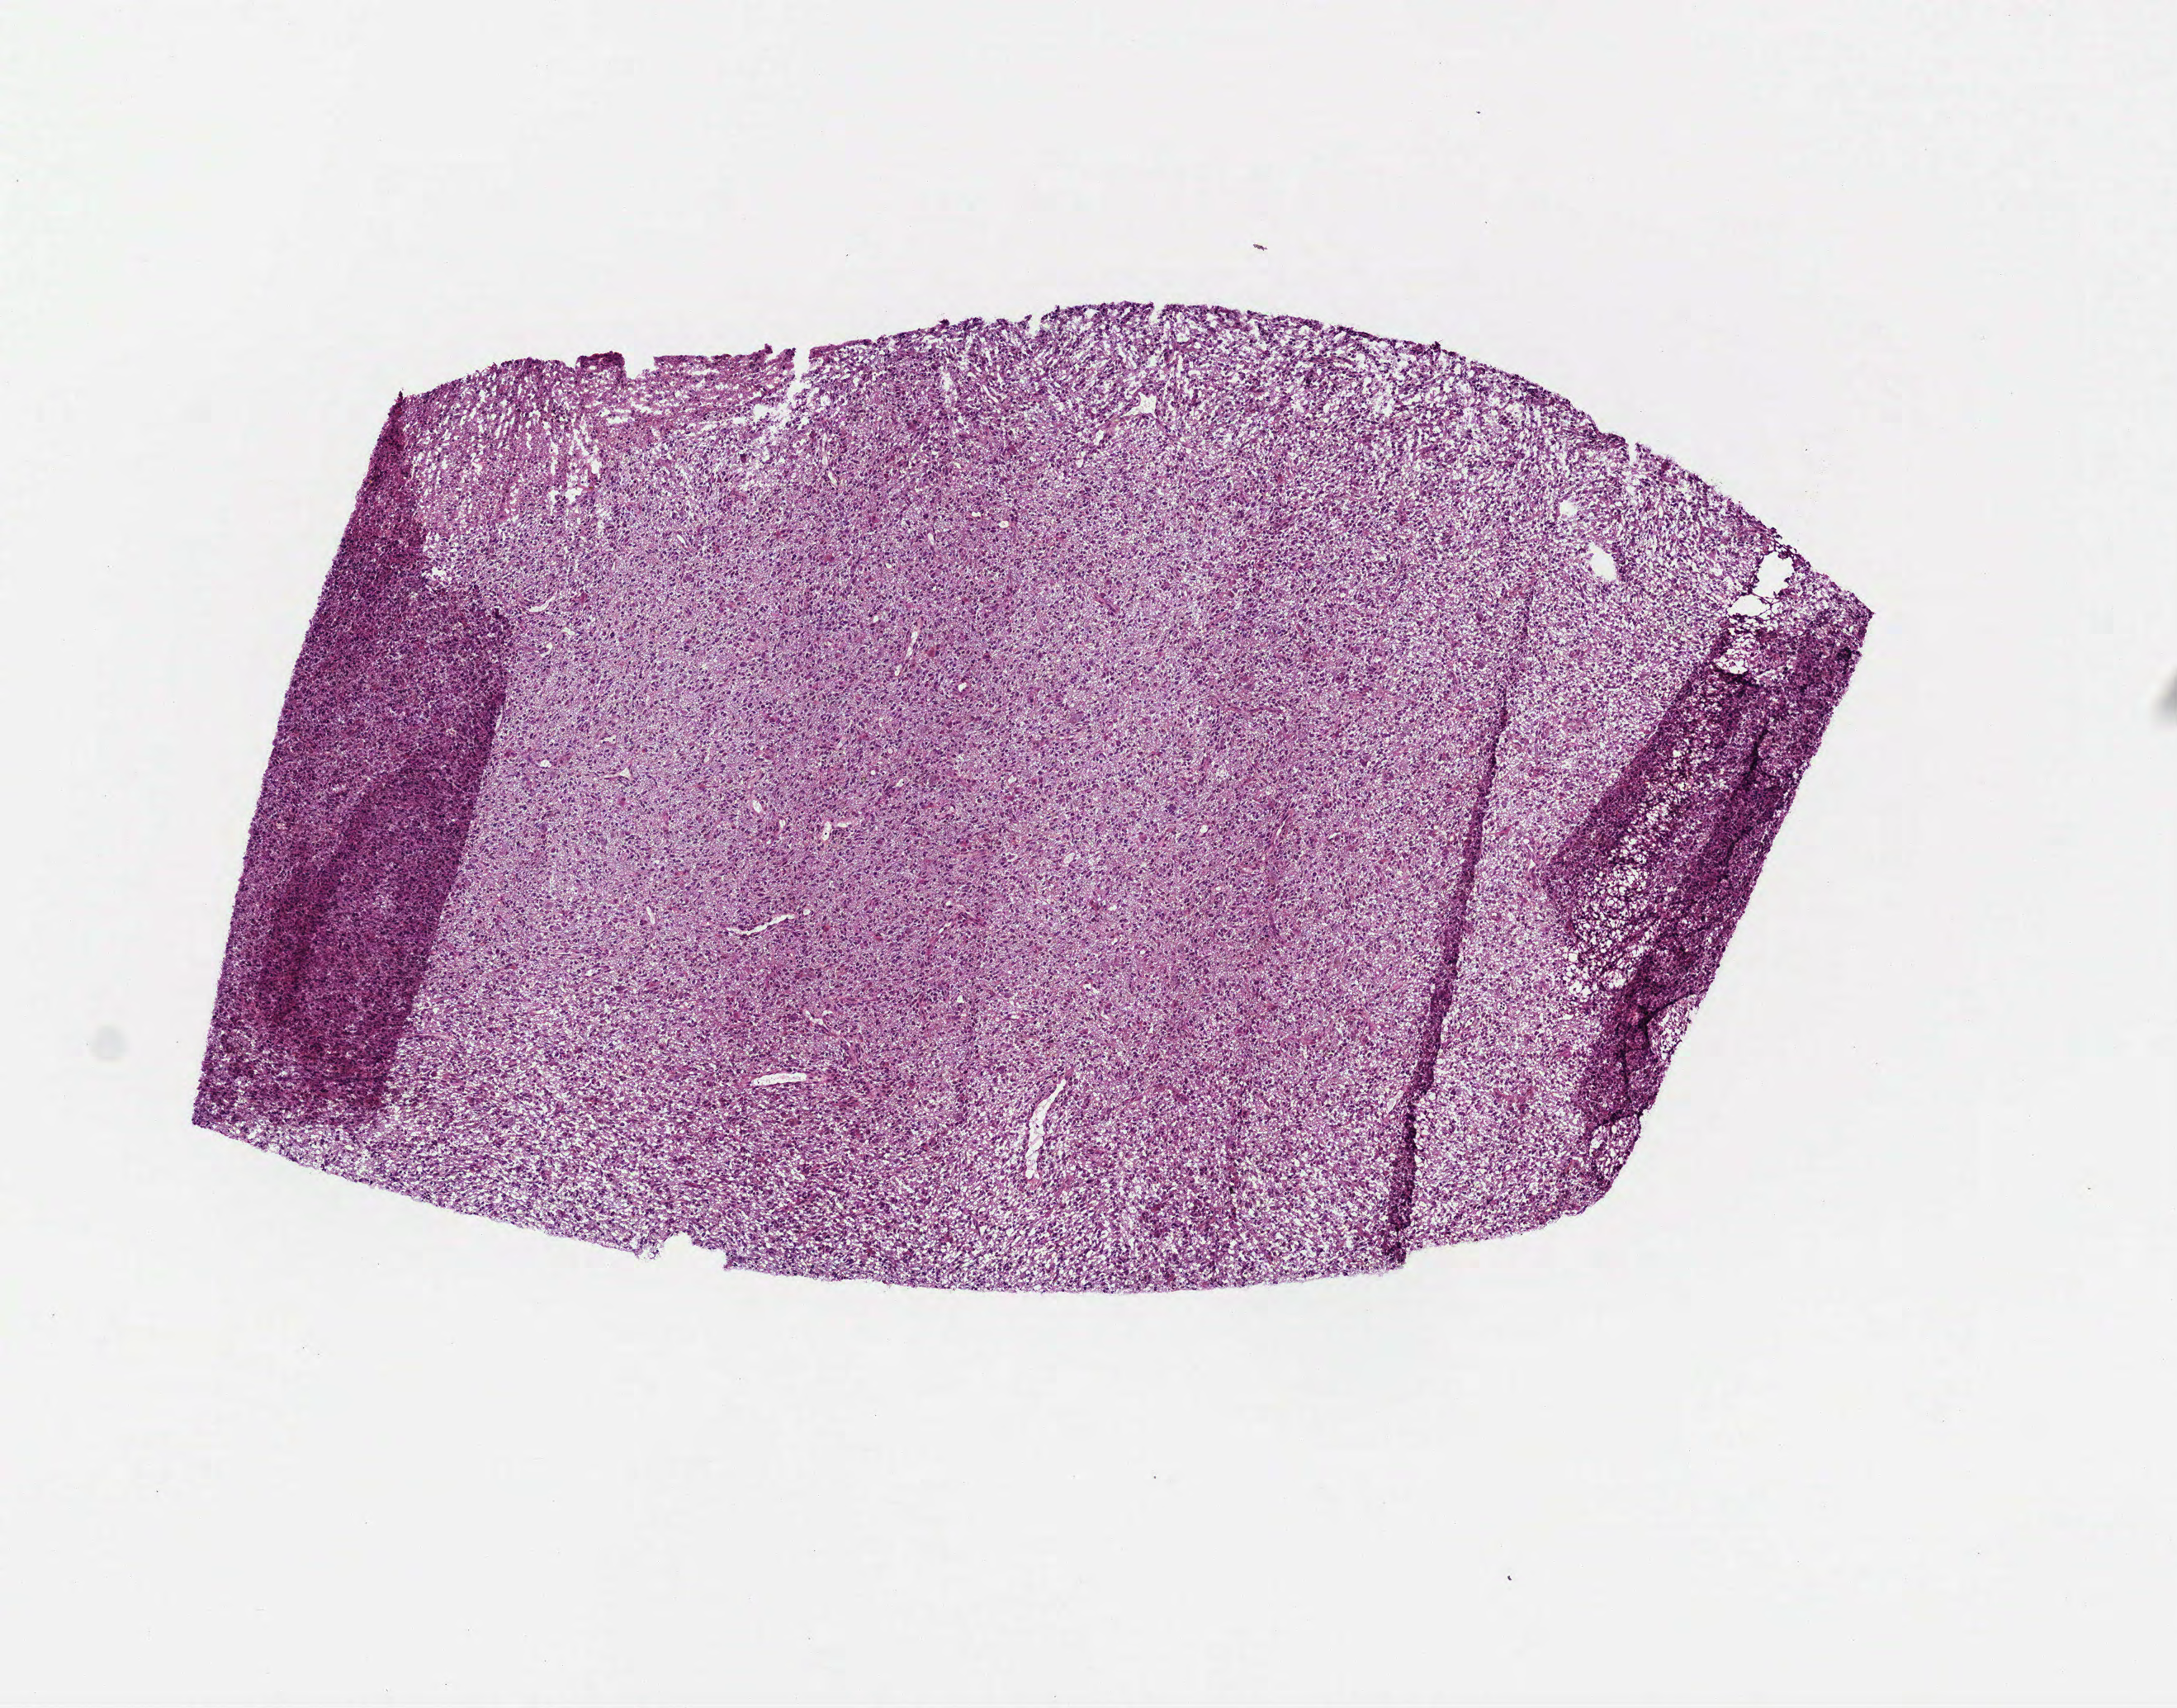
Digitized H&E-stained tissue section (whole slide), whole scanned area (about 5.3 x 4.2 mm, acquisition: 40x scan) shown as a low-resolution overview, frozen section, sample: primary tumour, brain. Female, age 50 years at initial diagnosis. Slide review estimates, as recorded: tumour cells 100%, tumour nuclei 85%, normal cells 0%, stromal cells 0%, necrosis 0%.
Histologic diagnosis: Glioblastoma.